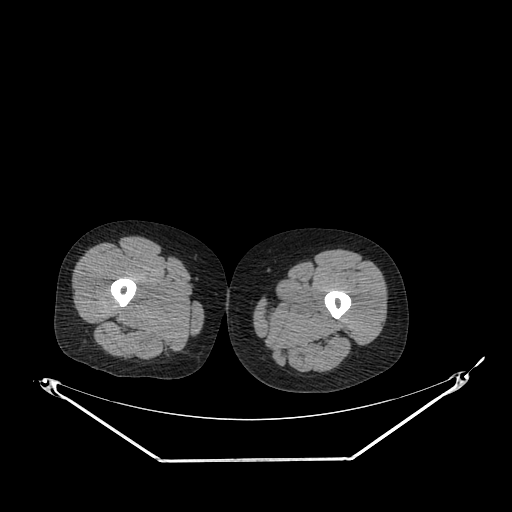
CT of an extremity soft-tissue mass (from a PET/CT study), one axial slice. Position 220 of 267 along the scan axis. Reconstruction kernel SOFT. 120 kVp. Soft-tissue window (W 400 / L 40 HU). 3.75 mm slice thickness. 512 × 512 image matrix, field of view 500 × 500 mm. Female patient. From the clinical record (not read from this slice): histological type: pleiomorphic leiomyosarcoma; grade: intermediate; site of the primary tumour: left thigh.
Annotated regions visible in this slice (expert contour drawn on MRI and transferred to this co-registered scan by the dataset authors):
- gross tumour volume including surrounding oedema: box from (x=267, y=297) to (x=323, y=318) px